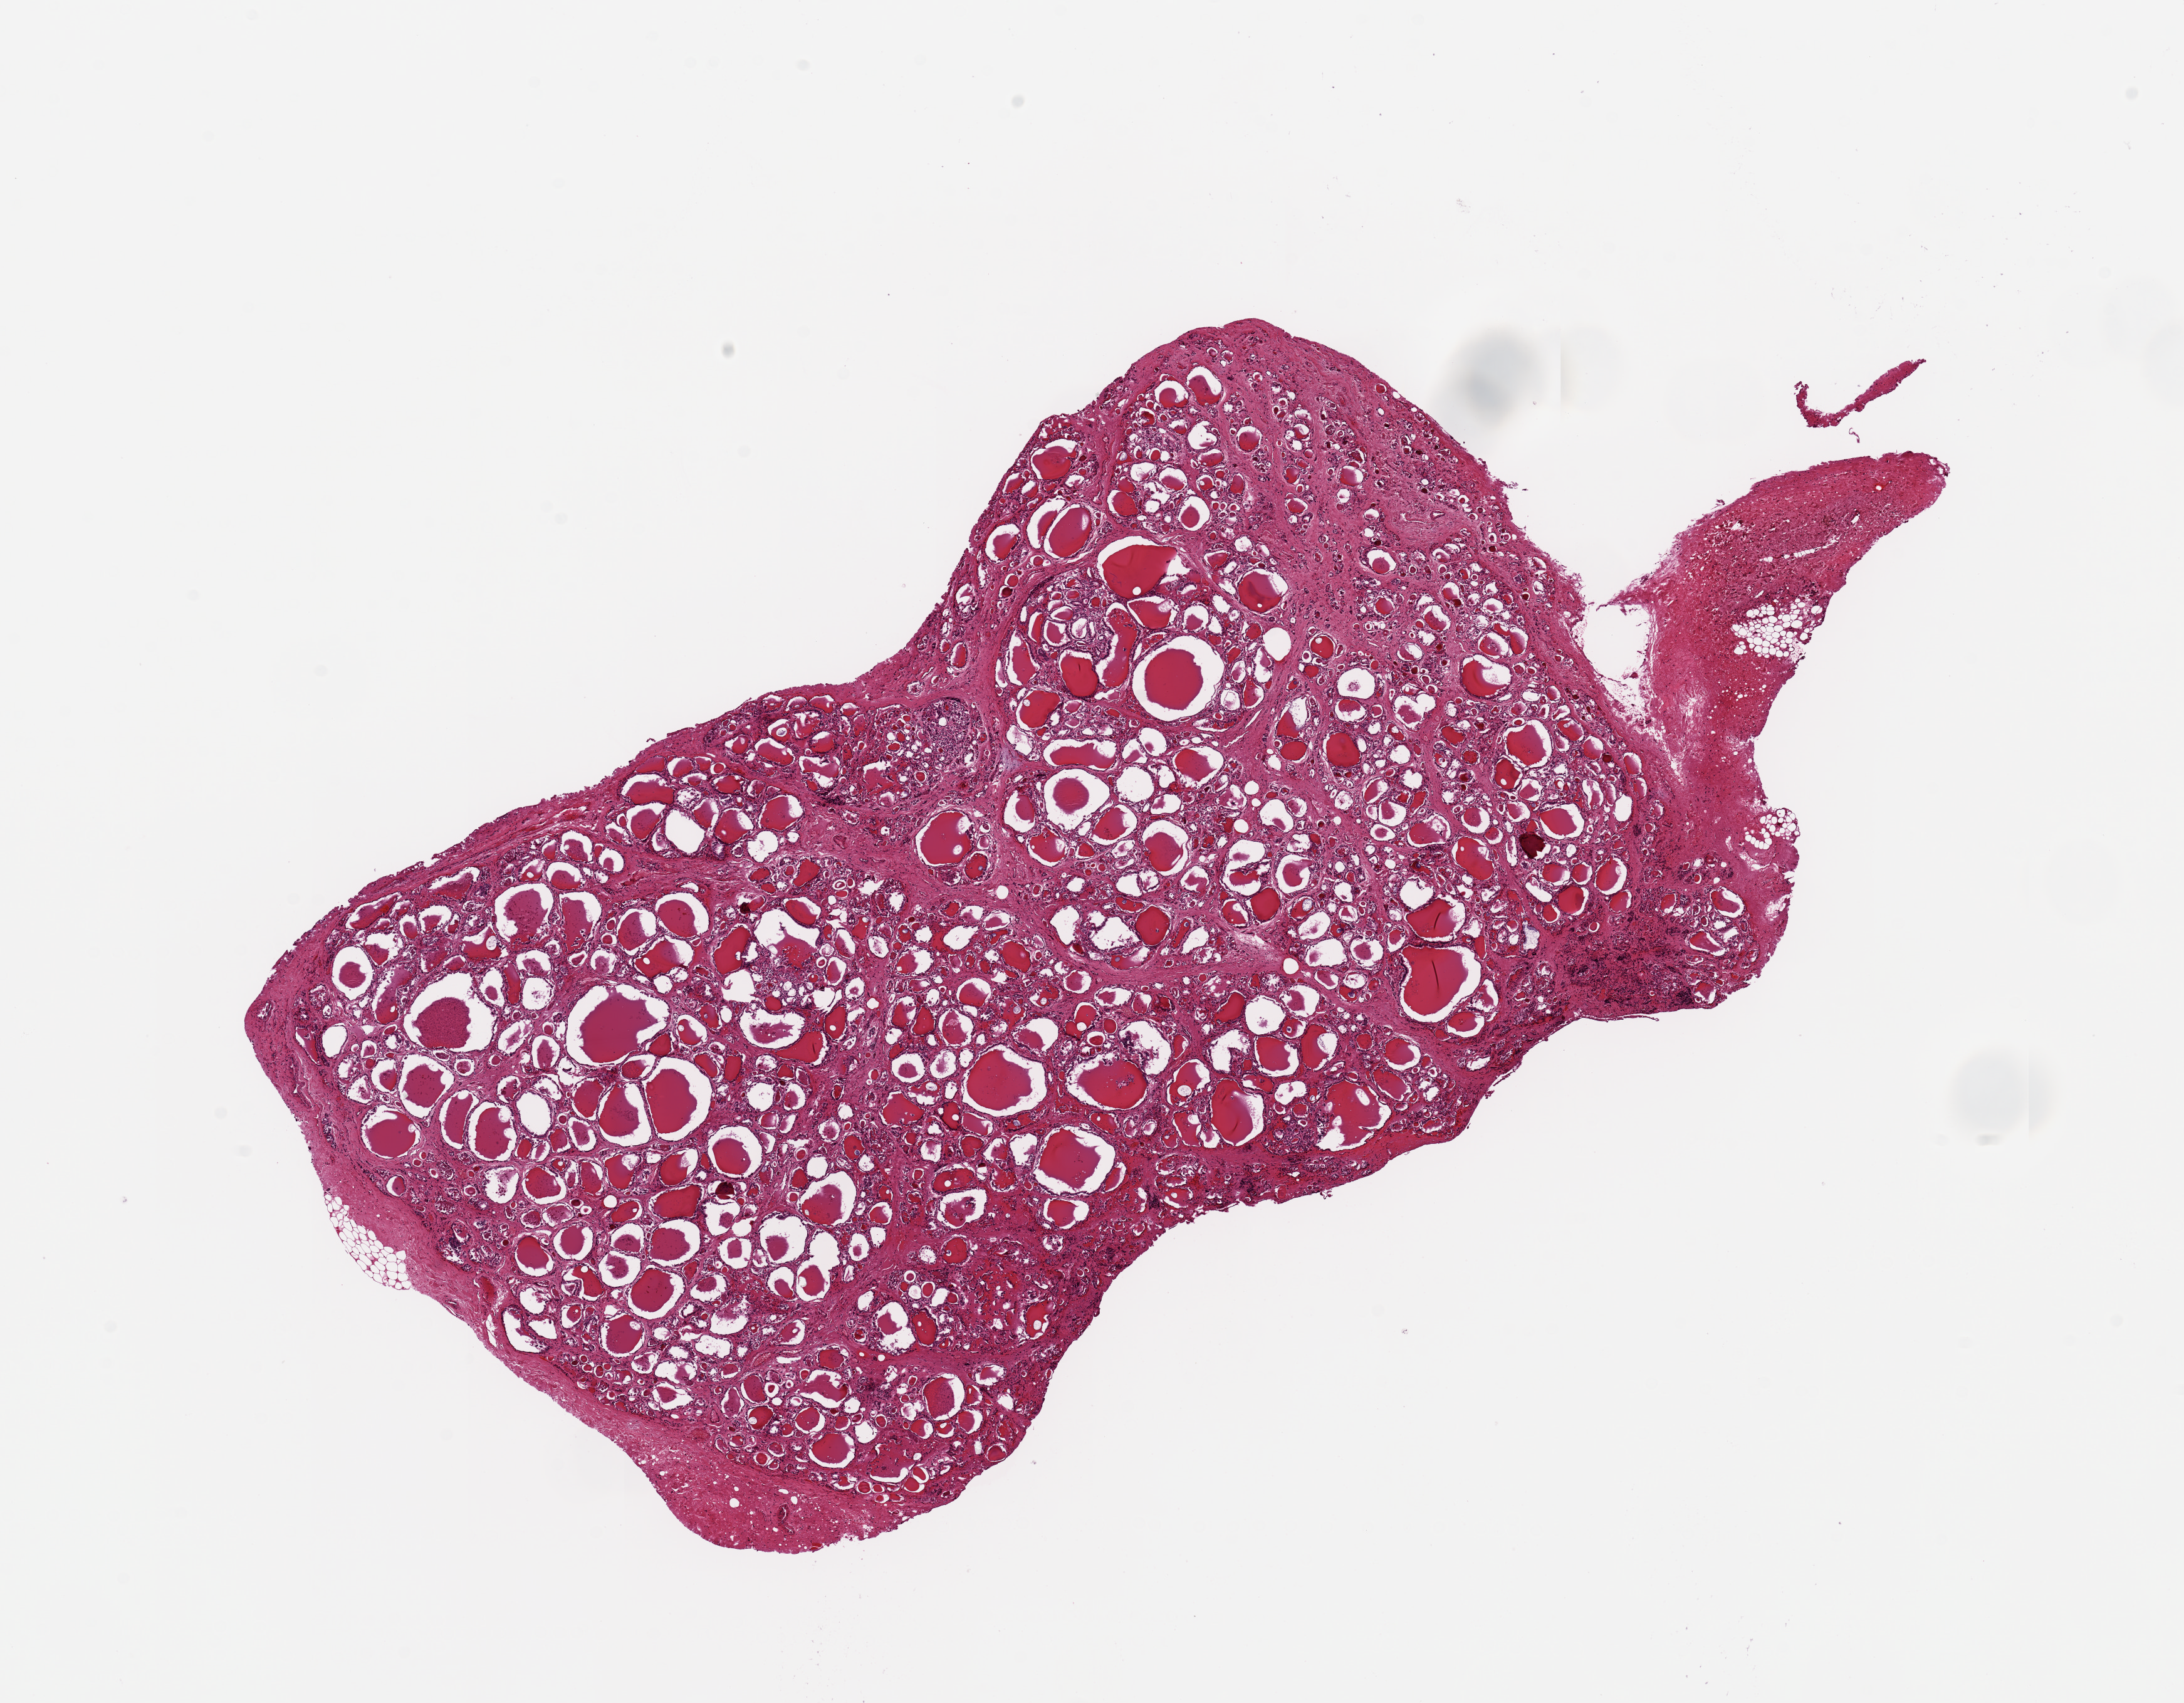
Whole-slide image, haematoxylin and eosin stain — whole scanned area (about 13.8 x 10.7 mm, acquisition: 20x scan) shown as a low-resolution overview, PAXgene-fixed paraffin-embedded (PFPE) section, section of thyroid (target tissue), donor tissue sample.
Review note (as recorded): 8x5mm. Regressive changes/fibrosis.